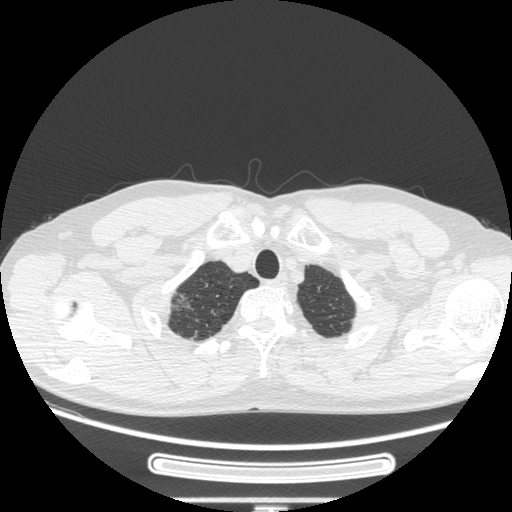
Chest CT, one axial slice. Position 240 of 269 along the scan axis. Reconstruction kernel STANDARD. Lung window (W 1500 / L -600 HU). 1.25 mm slice thickness. 512 × 512 image matrix, field of view 382 × 382 mm. Patient: male, 53 years. From the clinical record (not read from this slice): clinical TNM (as recorded): T1c N0 M0.
Outlined on this slice (rectangle marked by the reading radiologist):
- lung tumour (recorded histology: adenocarcinoma): bounding box [x1, y1, x2, y2] px = [163, 287, 191, 318]